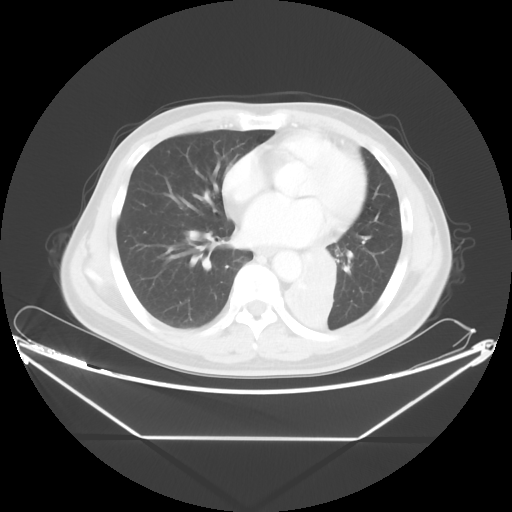
Chest CT, one axial slice. Slice 20 of 48 in the series (ordered by position). Reconstruction kernel STANDARD. 120 kVp. Lung window (W 1500 / L -600 HU). 5 mm slice thickness. 512 × 512 image matrix, field of view 438 × 438 mm. Patient: male, 58 years. Case-level facts recorded for this patient, not image findings: clinical TNM (as recorded): T3 N3 M0.
Outlined on this slice (bounding box drawn by a radiologist):
- lung tumour (recorded histology: squamous cell carcinoma): bounding box [x1, y1, x2, y2] px = [285, 242, 337, 328]